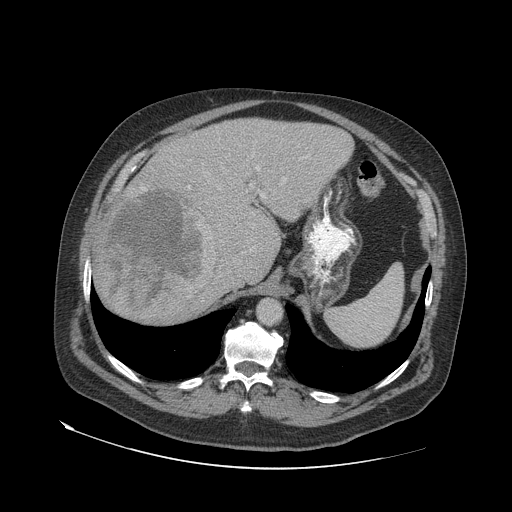
Contrast-enhanced abdominal CT (liver protocol), one axial slice. Slice 51 of 79 in the series (ordered by position). Reconstruction kernel STANDARD. 140 kVp. Soft-tissue window (W 400 / L 40 HU). 512 × 512 image matrix, field of view 480 × 480 mm. Case-level facts recorded for this patient, not image findings: diagnosis: hepatocellular carcinoma (patient treated with transarterial chemoembolisation; whether this scan precedes or follows treatment is not stated here); TNM stage (as recorded): Stage-IVA; Child-Pugh class: A; tumour differentiation: well differentiated; tumour nodularity: multinodular.
Annotated regions visible in this slice (semi-automatic segmentation, software-assisted and operator-edited):
- liver parenchyma outside the tumour (the mass and vessels are separate outlines, so this box may not span the whole liver): bounding box [x1, y1, x2, y2] px = [94, 118, 352, 320]
- mass: [98, 183, 220, 326]
- liver vessels: [188, 157, 307, 251]